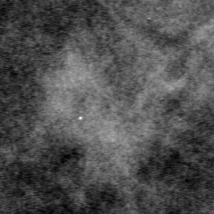
Region of interest cut from a scanned film mammogram (one marked finding); left breast; MLO view.
Finding: mass, shape oval, margins ill defined; BI-RADS assessment category 4; pathology (as recorded): malignant.